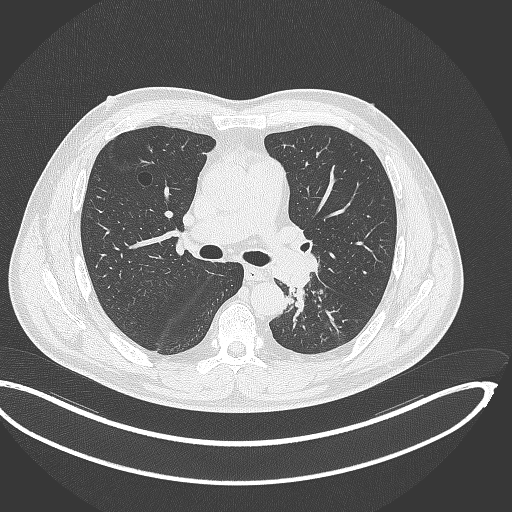
Chest CT, one axial slice; slice 214 of 362 in the series (ordered by position); reconstruction kernel B70f; 120 kVp; lung window (W 1500 / L -600 HU); 1 mm slice thickness; 512 × 512 image matrix, field of view 442 × 442 mm. Patient: male, 50 years. Case-level facts recorded for this patient, not image findings: clinical TNM (as recorded): T2a N3 M0.
Structures marked on this image (bounding box drawn by a radiologist):
- lung tumour (recorded histology: squamous cell carcinoma): bounding box <282,269,310,323> (left, top, right, bottom; pixels)